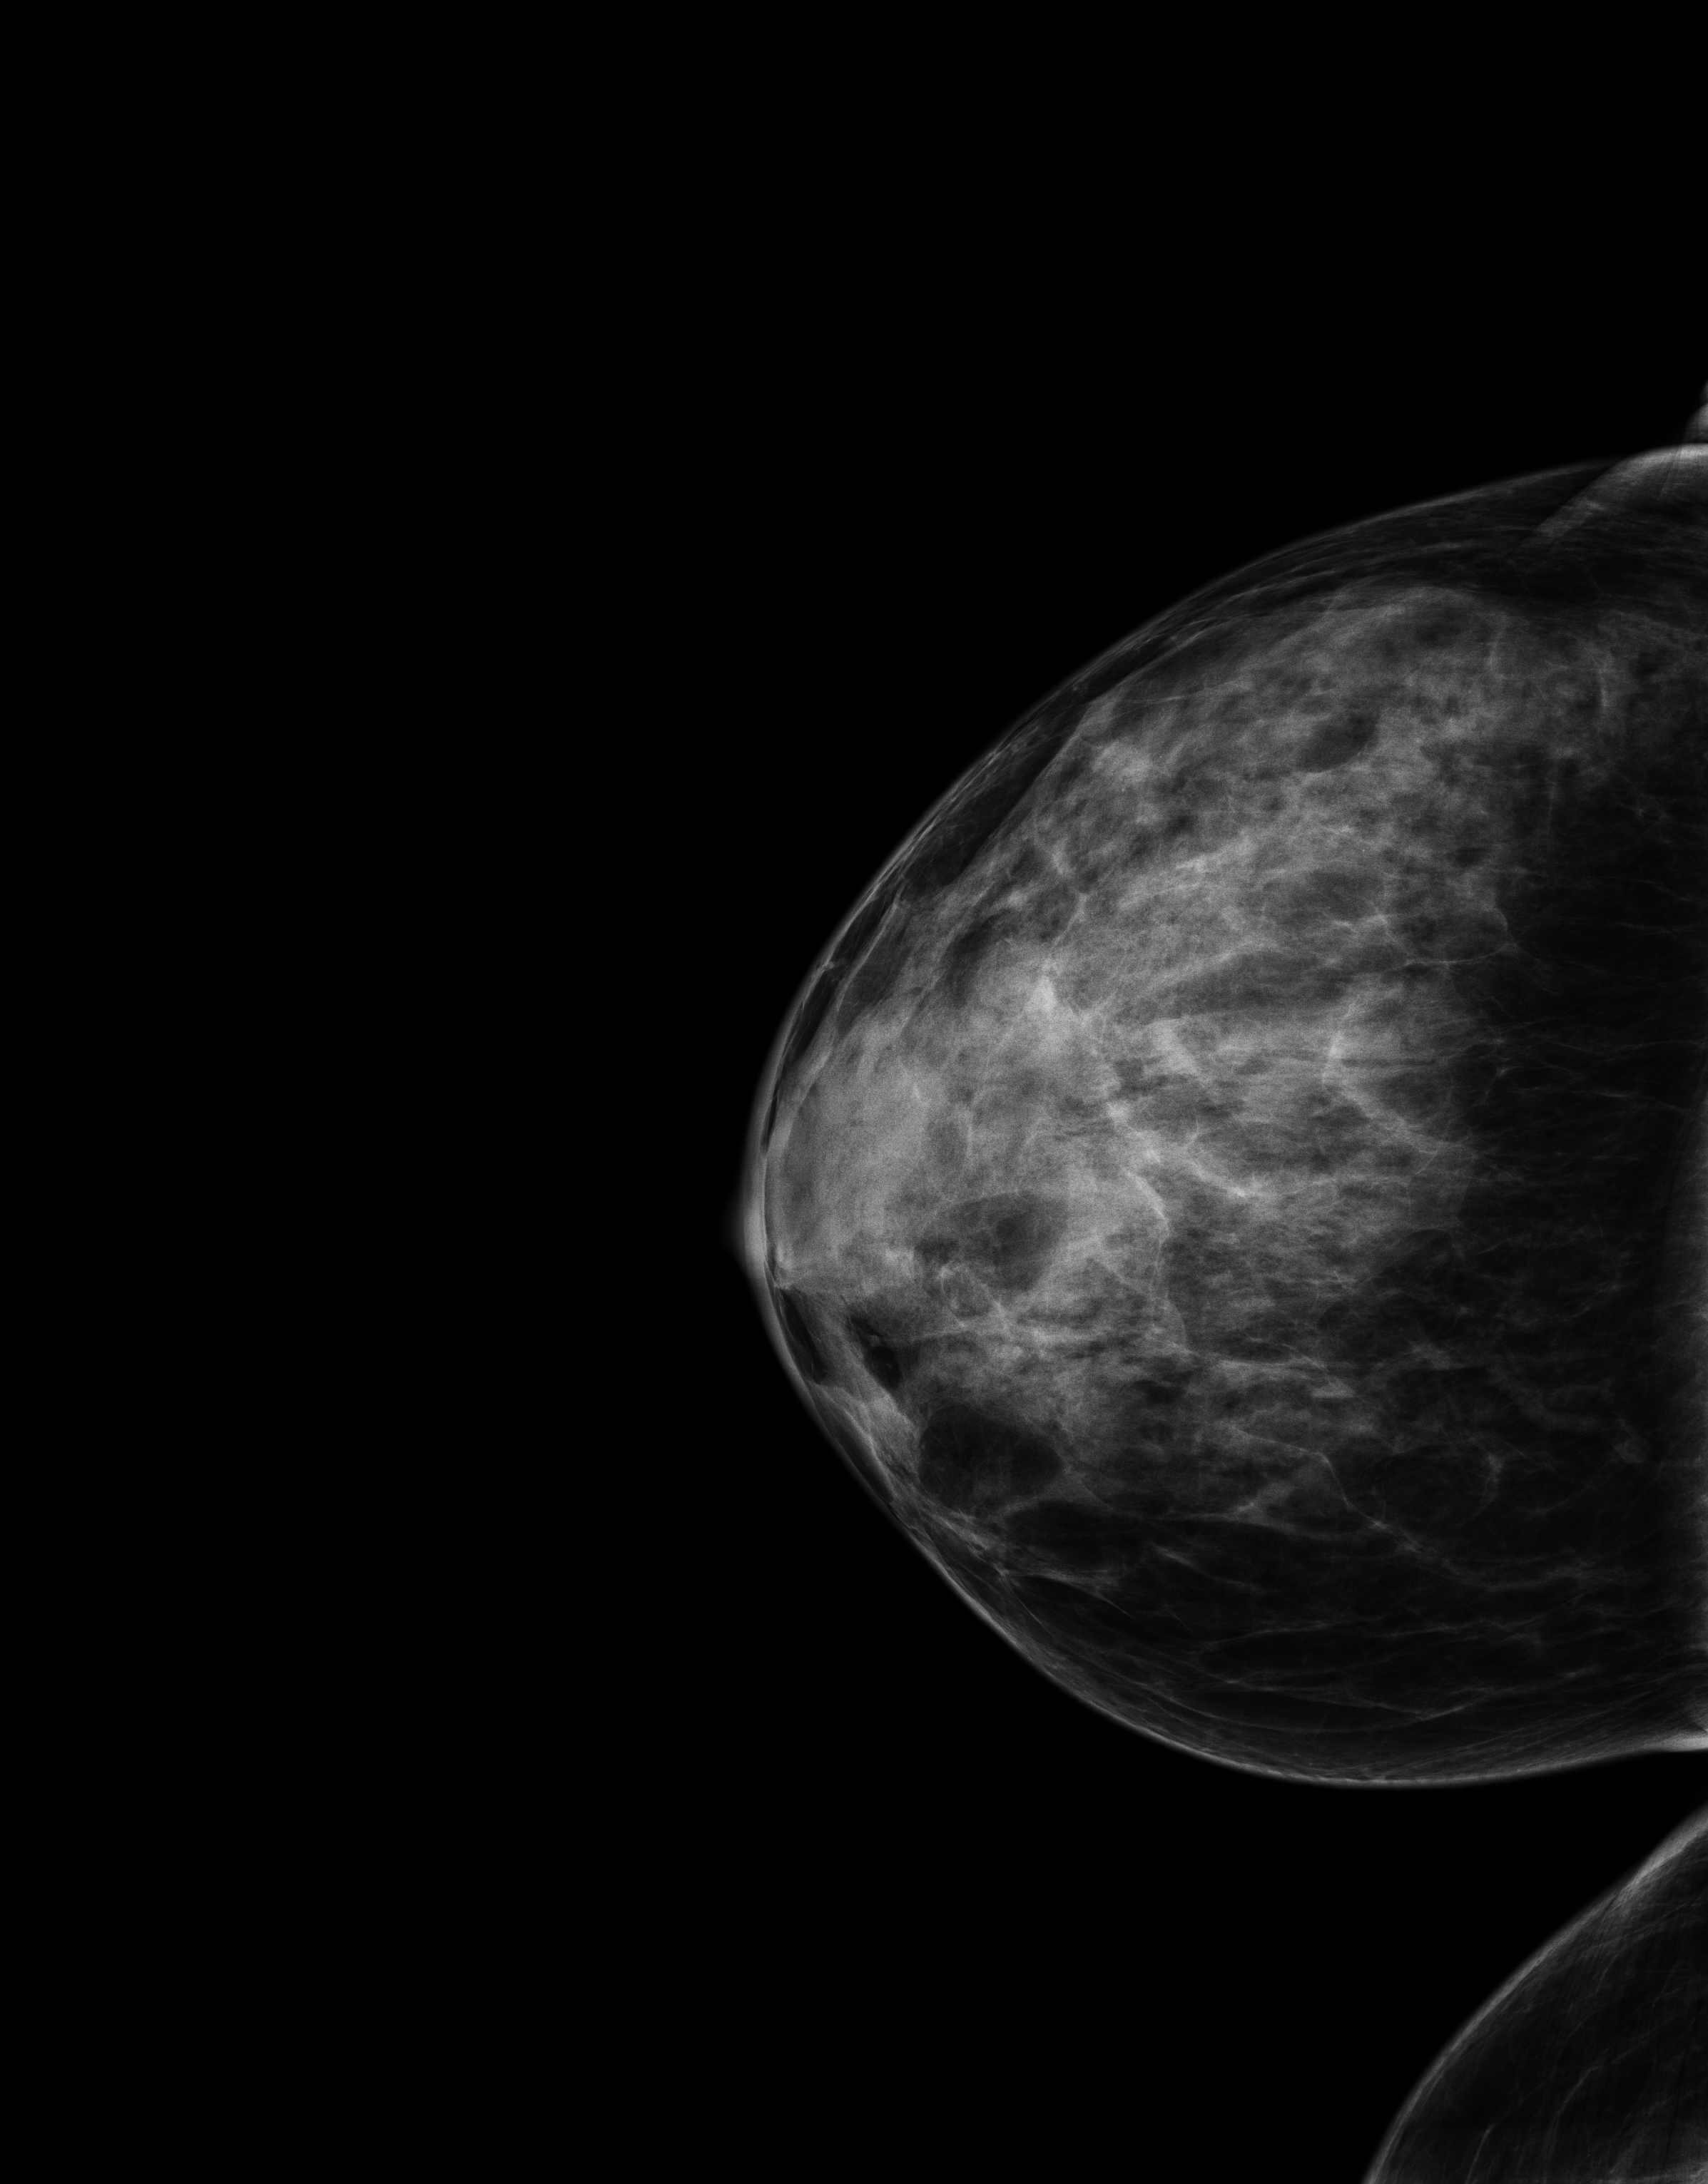
Digital mammogram (FFDM); right breast; cranio-caudal projection; screening examination; compressed breast thickness 38 mm. Female patient, age 48 years.
BI-RADS breast density category at the screening exam (both breasts, scale 1–4): 4. Final BI-RADS category for the screening round (tomosynthesis exam, both breasts): category 2. Recall: recalled for additional imaging after this screen.